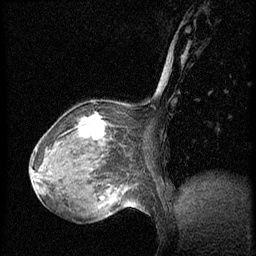
Breast MRI (dynamic contrast-enhanced), one sagittal slice; position 23 of 56 along the scan axis; dynamic contrast-enhanced series, image 2 of 3 at this slice position (ordered by acquisition); 1.5 T; TE 4.2 ms, TR 20.4 ms; 2 mm slice thickness; 256 × 256 image matrix, field of view 200 × 200 mm. Patient: female, 64 years. Case-level facts recorded for this patient, not image findings: setting: breast cancer imaged before/during neoadjuvant chemotherapy; receptor status: HR-positive, HER2-negative.
Structures marked on this image (semi-automatically segmented with operator editing):
- analysis volume of interest (the breast-tissue region the enhancement analysis was run in; not a lesion): bounding box (x1, y1, x2, y2) in pixels: (48, 101, 139, 186)
- tumour enhancement mask (voxels above the 70 % enhancement threshold inside the analysis volume of interest): (78, 114, 106, 140)